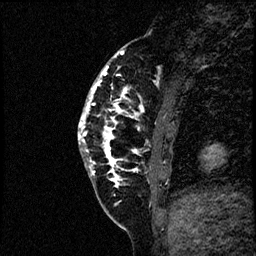
Breast MRI (dynamic contrast-enhanced), one sagittal slice. Dynamic contrast-enhanced study with each time point stored as its own series, time point 2 of 4 at this slice position (early post-contrast, ordered by acquisition time). 1.5 T. TE 4.2 ms, TR 17.6 ms. 2 mm slice thickness. 256 × 256 image matrix. Patient: female, 40 years. From the clinical record (not read from this slice): setting: breast cancer imaged before/during neoadjuvant chemotherapy; receptor status: HER2-positive.
Outlined on this slice (semi-automatically segmented with operator editing):
- analysis volume of interest (the breast-tissue region the enhancement analysis was run in; not a lesion): bounding box [x1, y1, x2, y2] px = [79, 56, 197, 205]
- tumour enhancement mask (voxels above the 100 % enhancement threshold inside the analysis volume of interest): [79, 65, 145, 186]